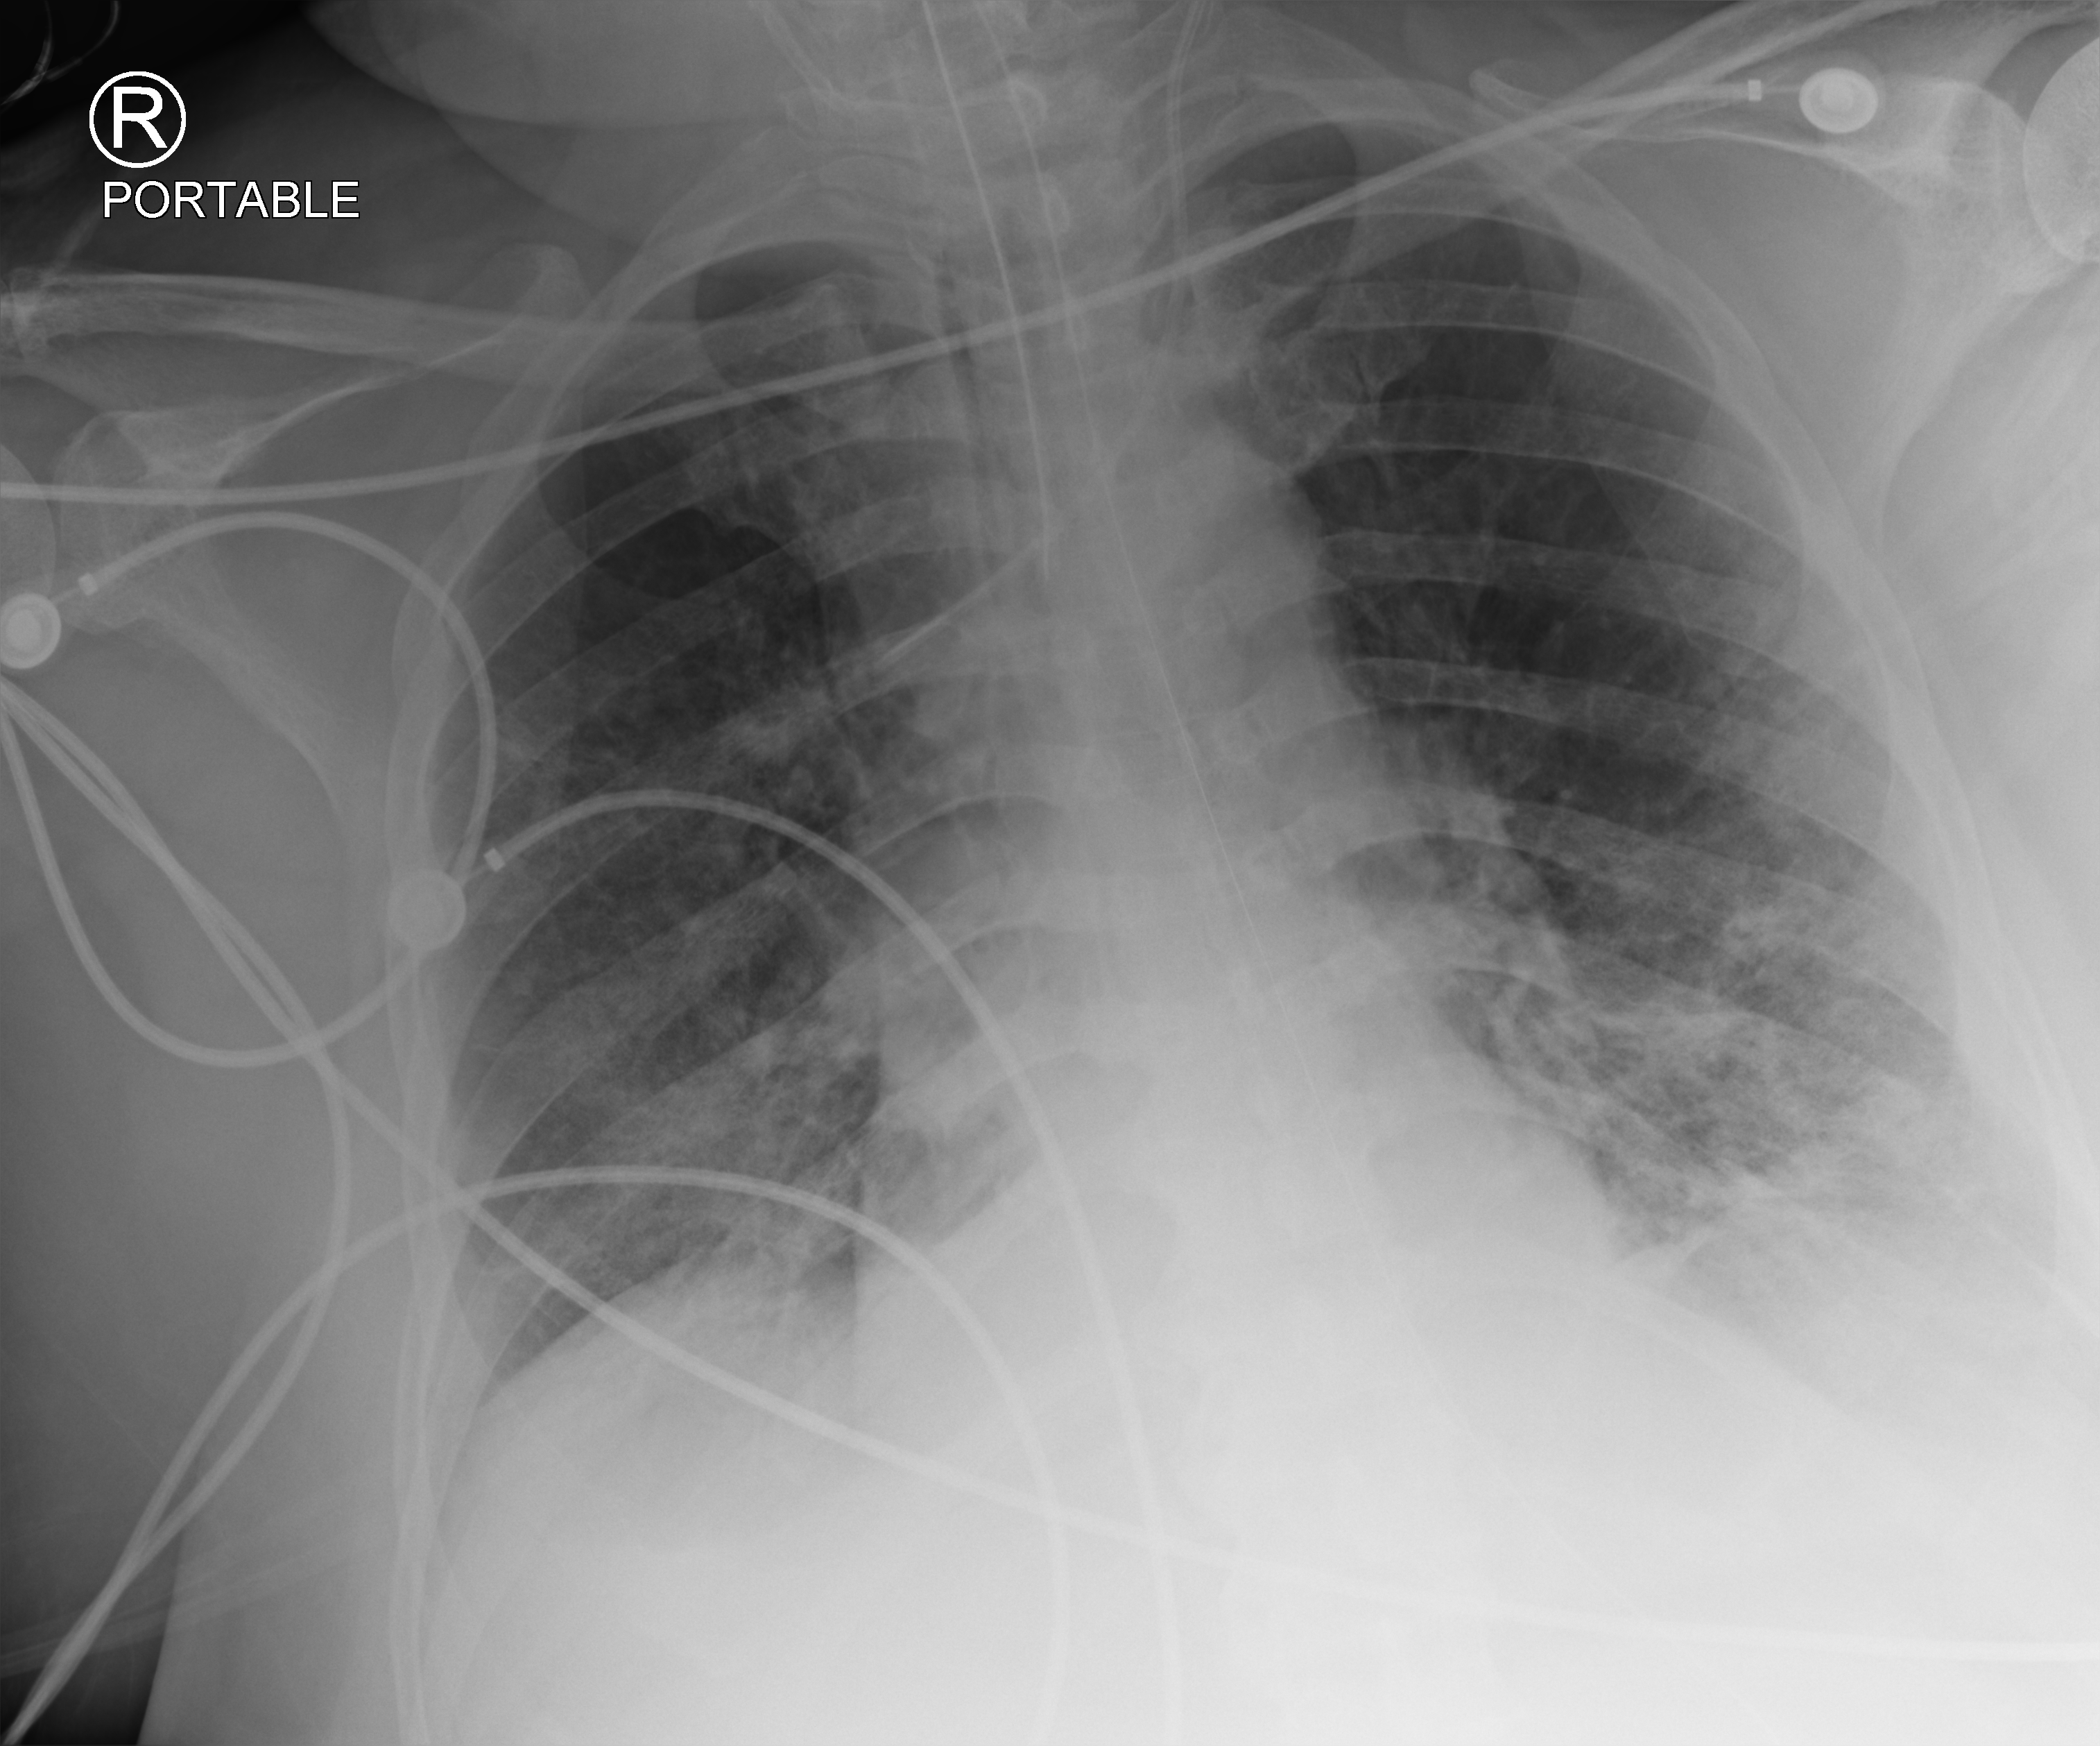
Chest X-ray (portable); anteroposterior (AP) projection. Patient hospitalised with COVID-19, aged 18–59 years.
Admission-level facts for this patient (not findings on this image; timing relative to this image not recorded):
- admitted to intensive care during this hospital stay: yes